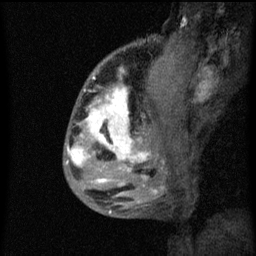
Breast MRI (dynamic contrast-enhanced), one sagittal slice. Slice 20 of 60 in the series (ordered by position). Dynamic contrast-enhanced series, image 2 of 3 at this slice position (ordered by acquisition). 1.5 T. TE 4.2 ms, TR 8 ms. 2 mm slice thickness. 256 × 256 image matrix, field of view 180 × 180 mm. Female patient, age 50 years.
Annotated regions visible in this slice (semi-automatic segmentation, software-assisted and operator-edited):
- analysis volume of interest (the breast-tissue region the enhancement analysis was run in; not a lesion): bounding box (x1, y1, x2, y2) in pixels: (66, 64, 141, 187)
- tumour enhancement mask (voxels above the 70 % enhancement threshold inside the analysis volume of interest): (66, 72, 141, 183)